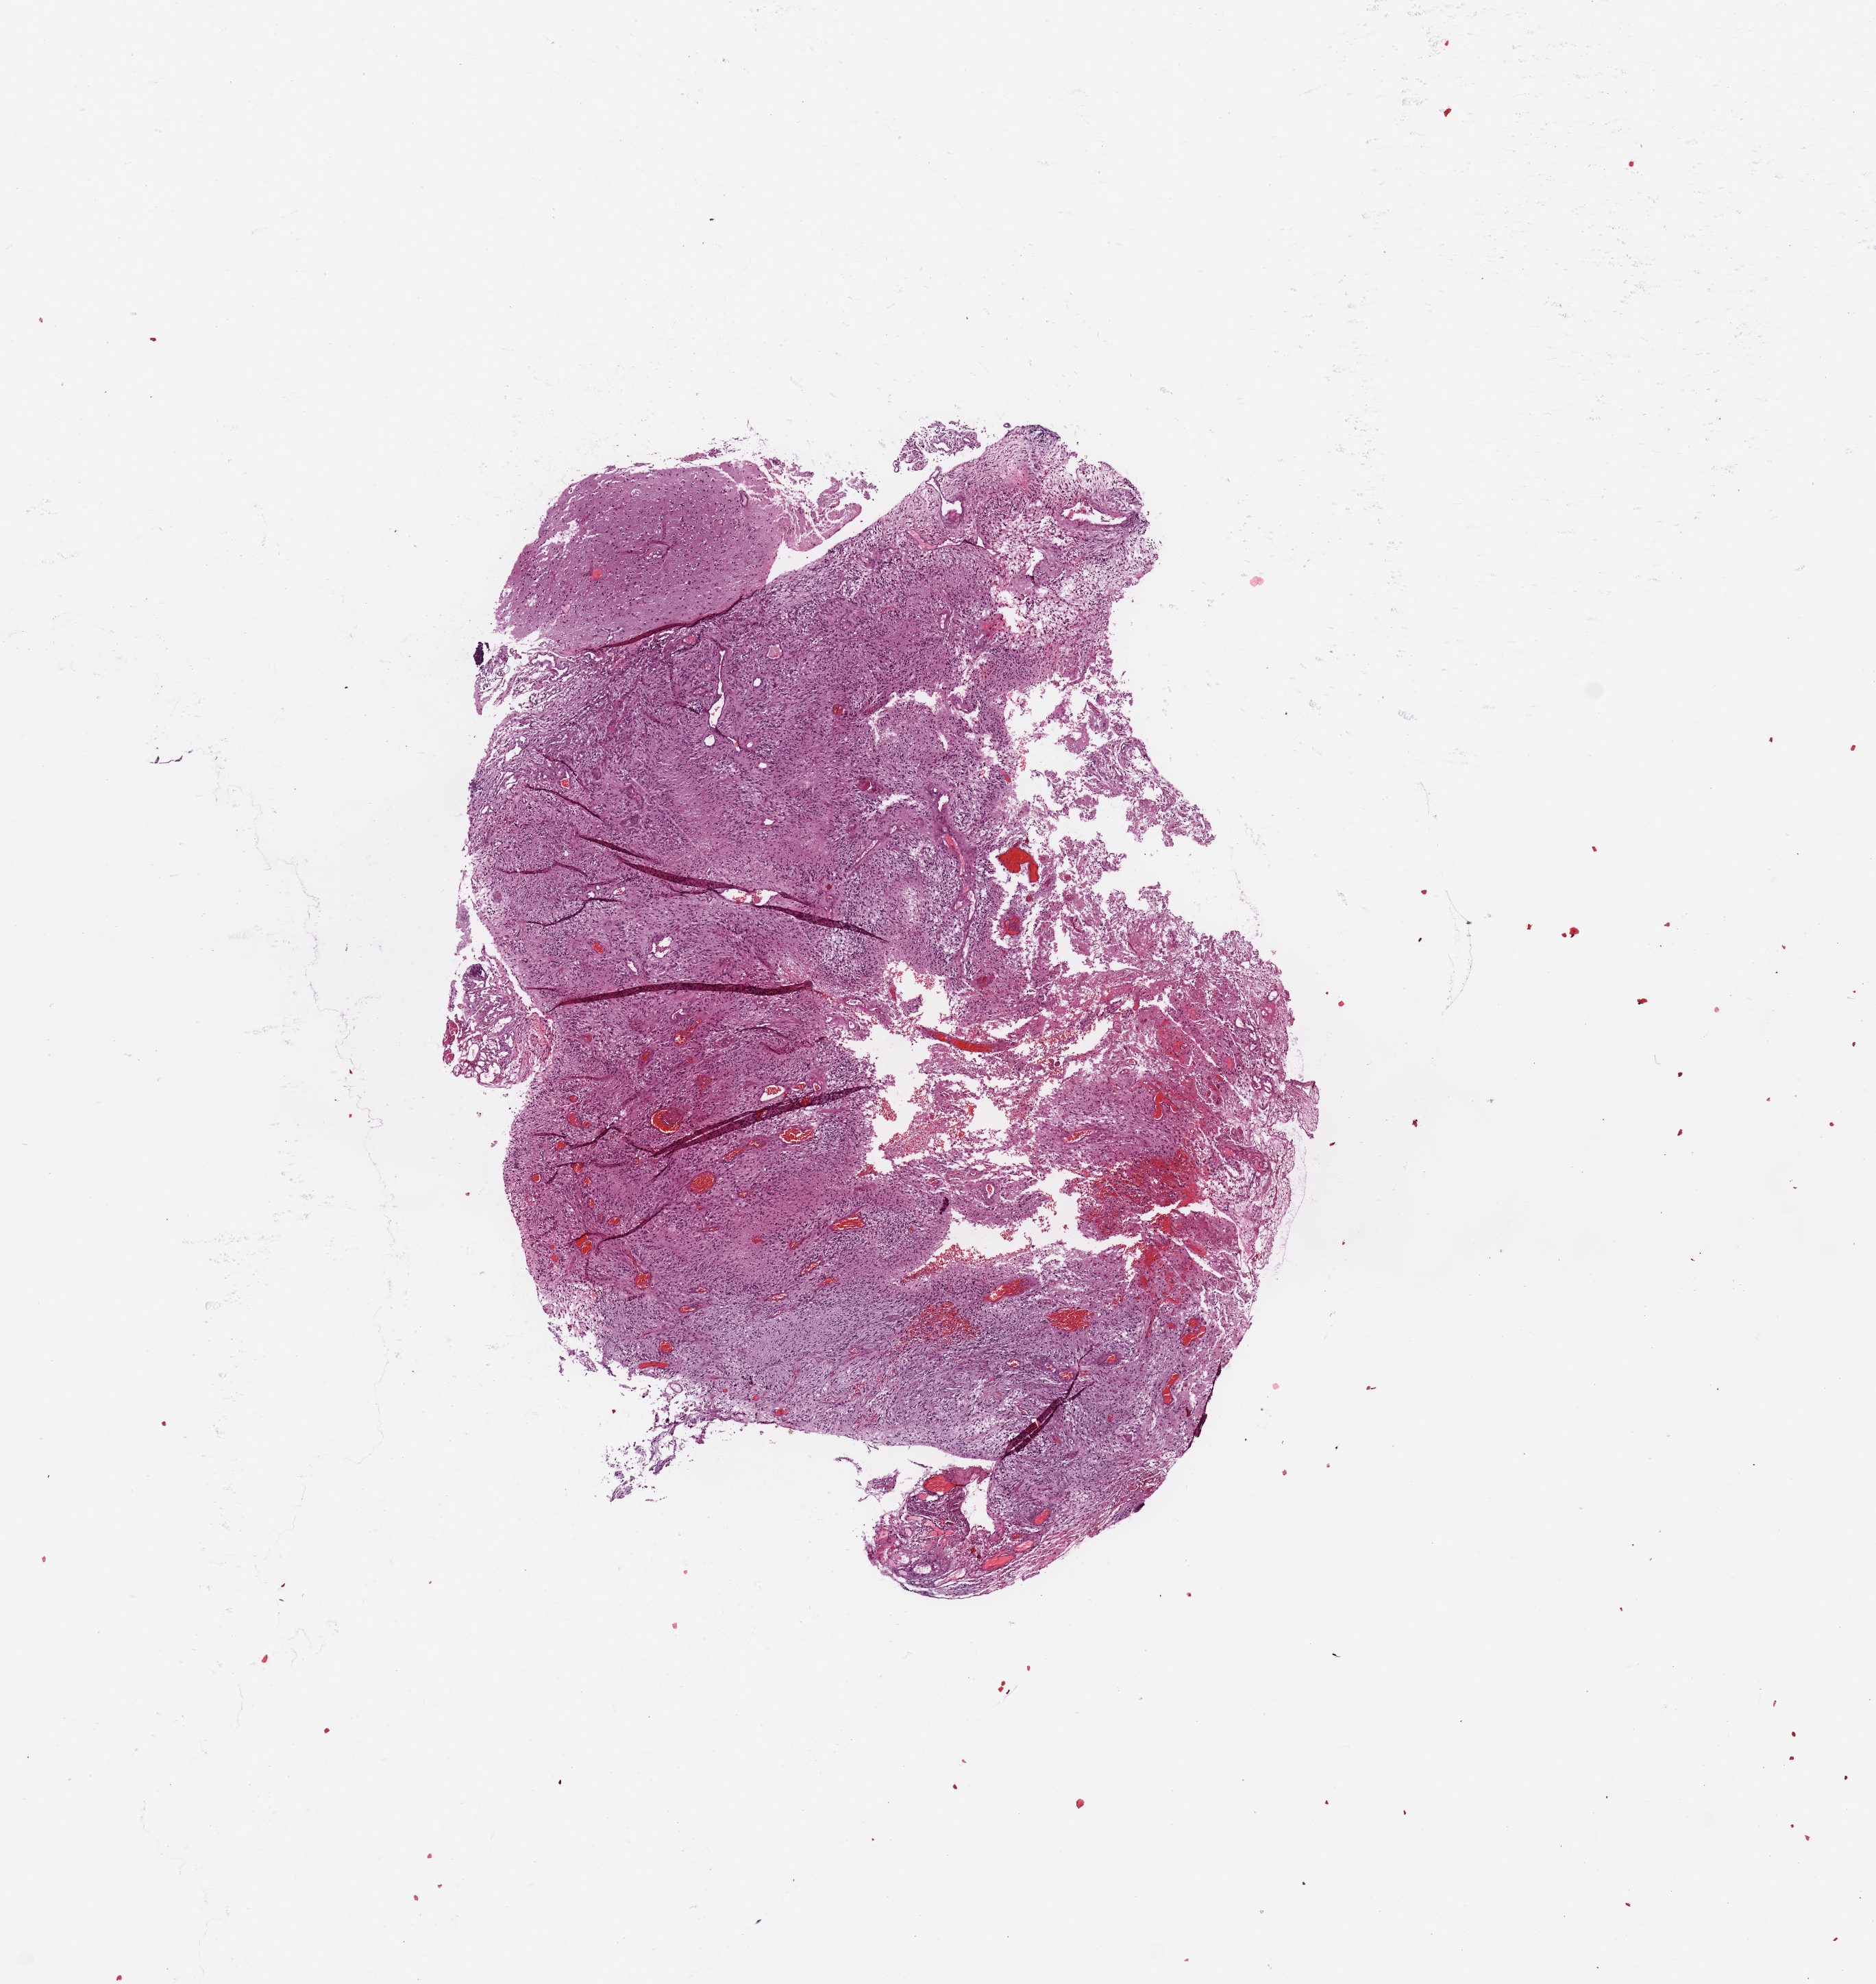
Digitized Hematoxylin and eosin (H&E) stained tissue section (whole slide), a low-resolution overview of the entire scanned area, about 10.8 x 11.5 mm (slide scanned at 20x). Tumour tissue sample, sampled site: brain. 54-year-old female patient. Pathologist review of this section (percent, as recorded): tumour nuclei 70%, necrosis 5%.
• histologic diagnosis: Glioblastoma